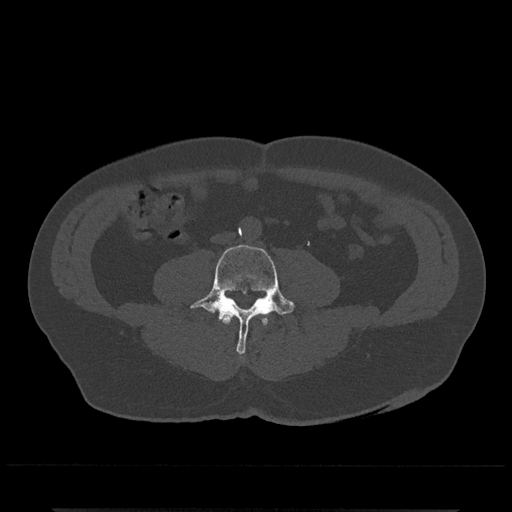
CT including the spine, one axial slice; position 155 of 797 along the scan axis; reconstruction kernel Br40s/3; bone window (W 1800 / L 400 HU); 0.5 mm slice thickness; 512 × 512 image matrix, field of view 393 × 393 mm. Male patient, age 67 years. Case-level facts recorded for this patient, not image findings: primary cancer: prostate.
Annotated regions visible in this slice (semi-automatically segmented with operator editing):
- L3 vertebra: box from (x=221, y=313) to (x=268, y=325) px
- L4 vertebra: (x=190, y=244)–(x=295, y=355)